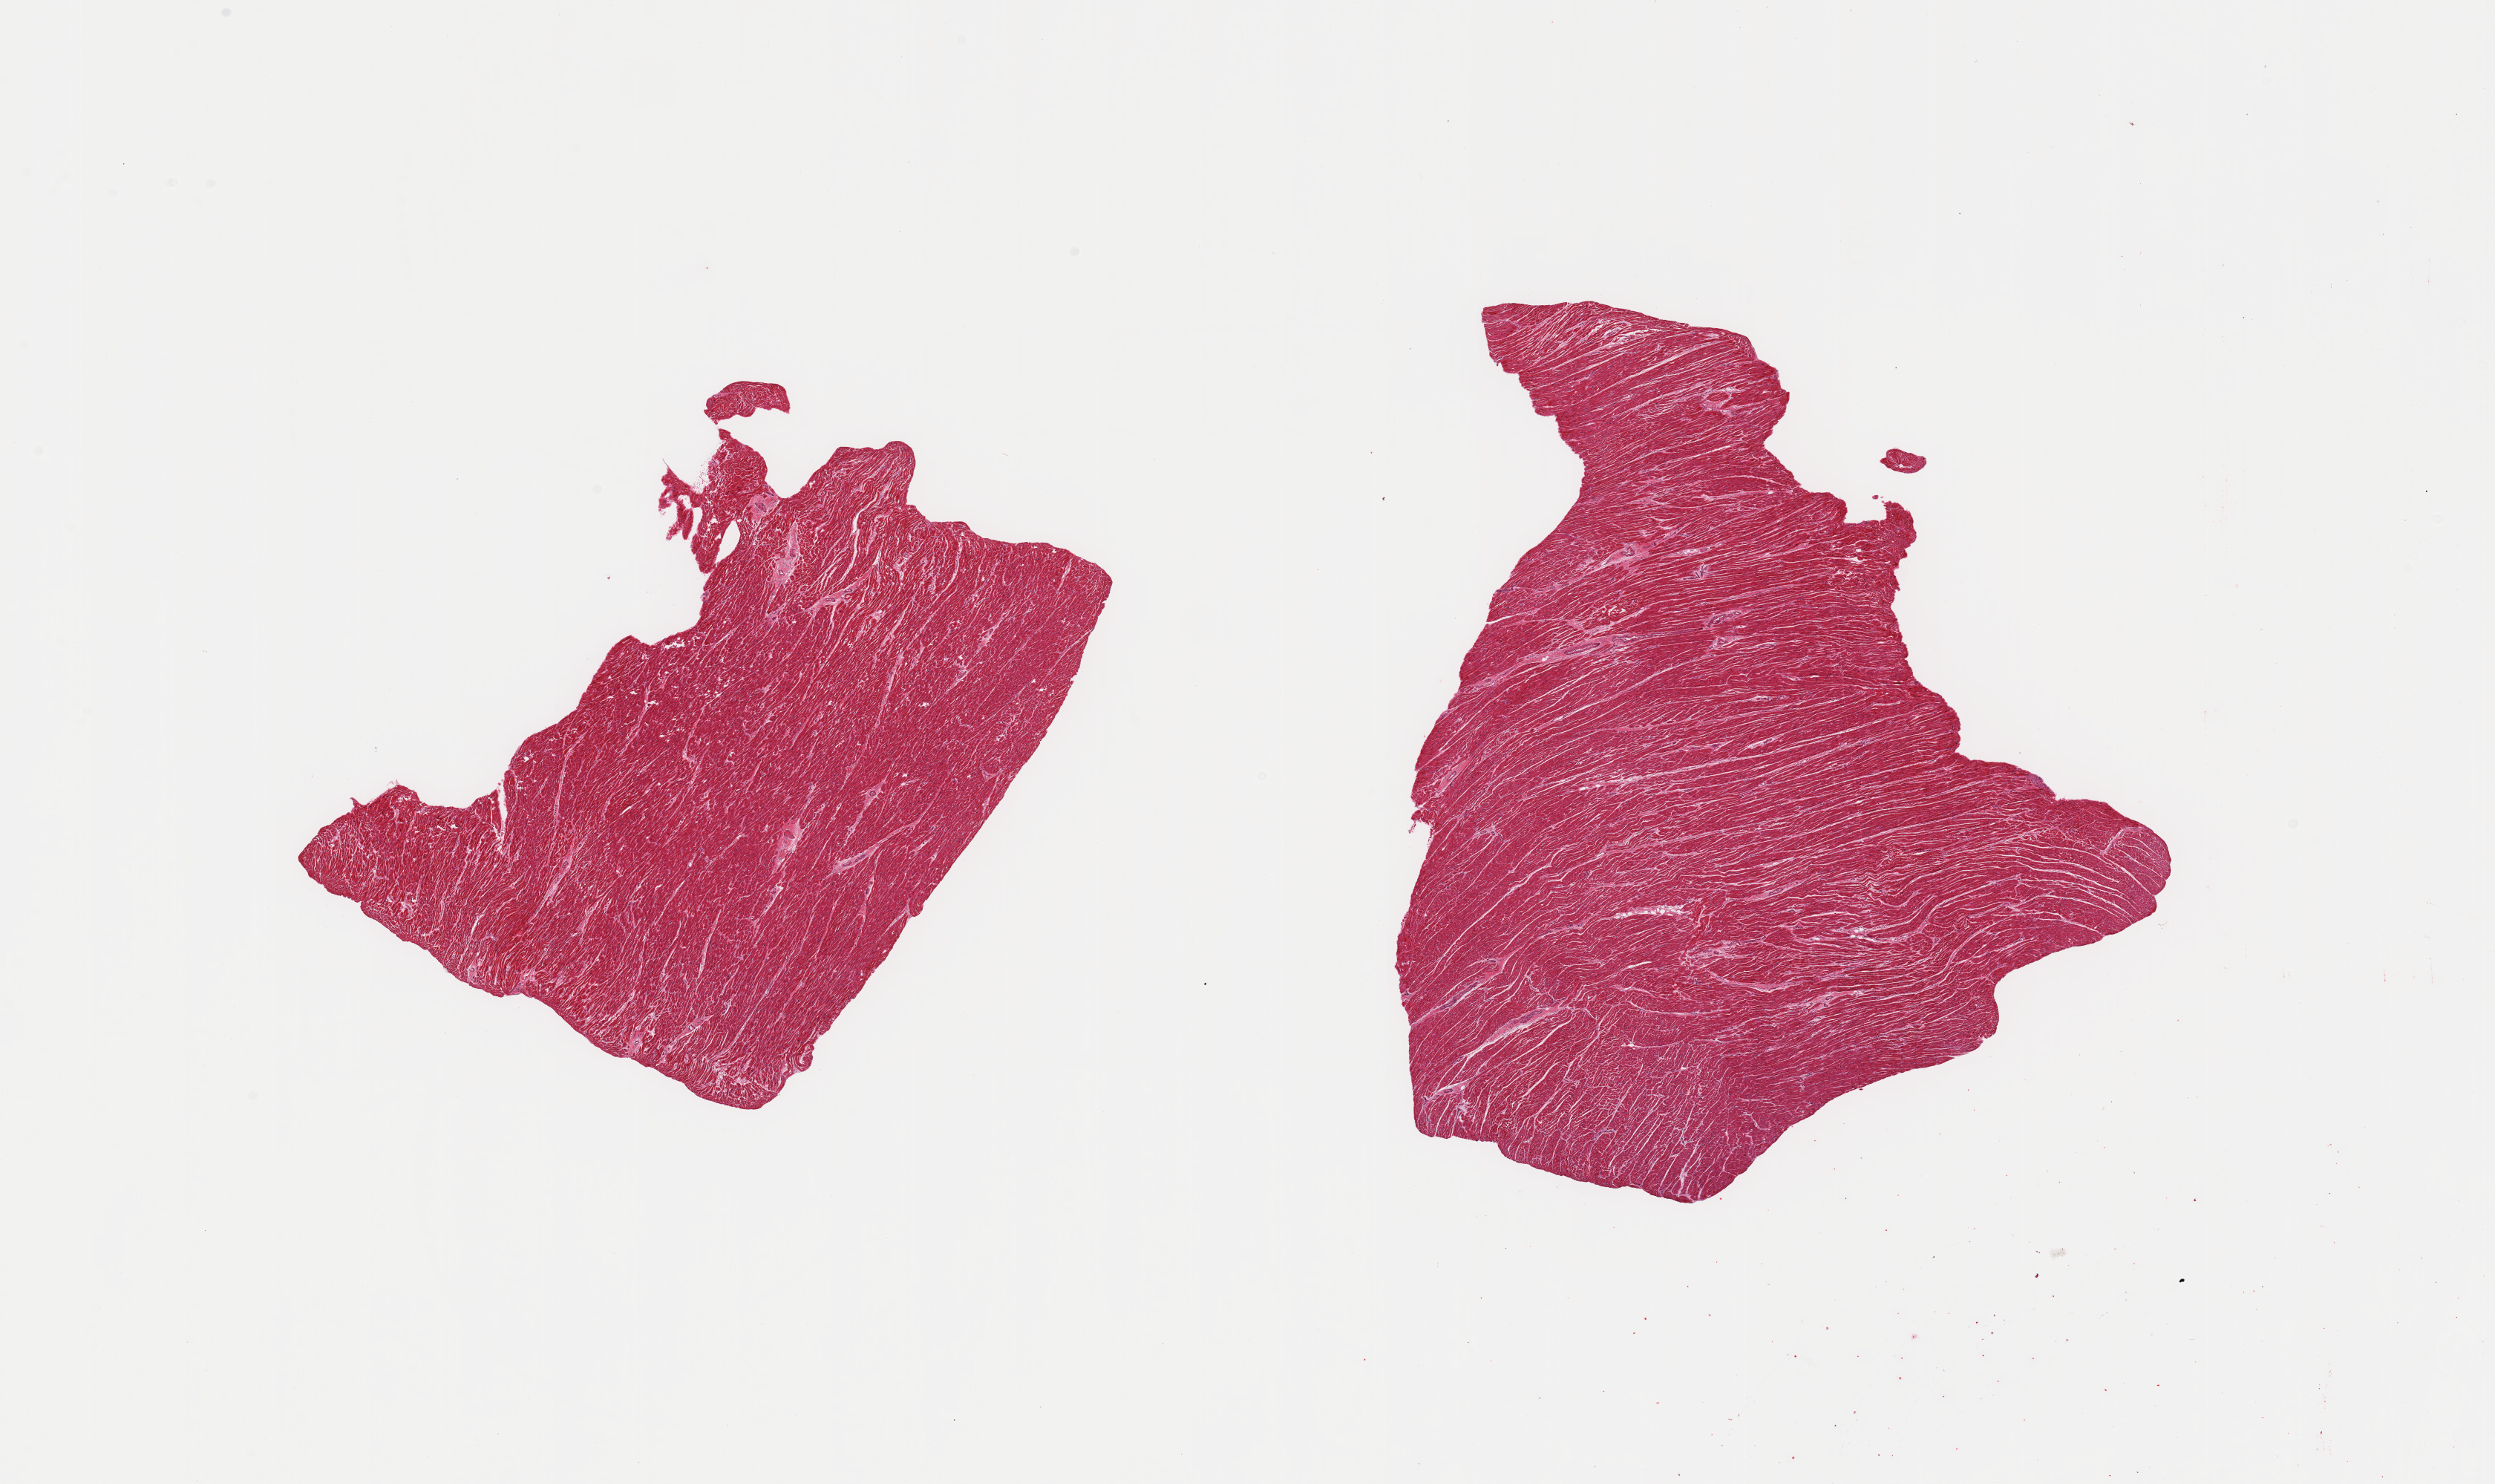
H&E whole-slide image, whole scanned area (about 26.6 x 15.8 mm, from a 20x scan) shown as a low-resolution overview, PAXgene-fixed, paraffin-embedded tissue, target tissue: heart, tissue donor sample.
• reviewer comment on this tissue sample: 2 pieces; no lesions; no fat